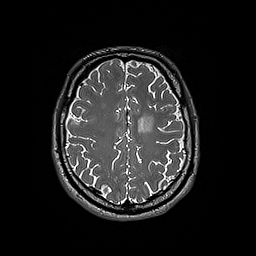
Brain MRI from a brain-tumour surgery series, one axial slice; slice 62 of 192 in the series (ordered by position); 256 × 256 image matrix, field of view 250 × 250 mm. Case-level facts recorded for this patient, not image findings: histopathology: Oligodendroglioma; WHO grade: 3; IDH mutation: yes; tumour location: Left Frontal.
Outlined on this slice (manually delineated by an expert):
- tumour: box from (x=138, y=116) to (x=154, y=132) px